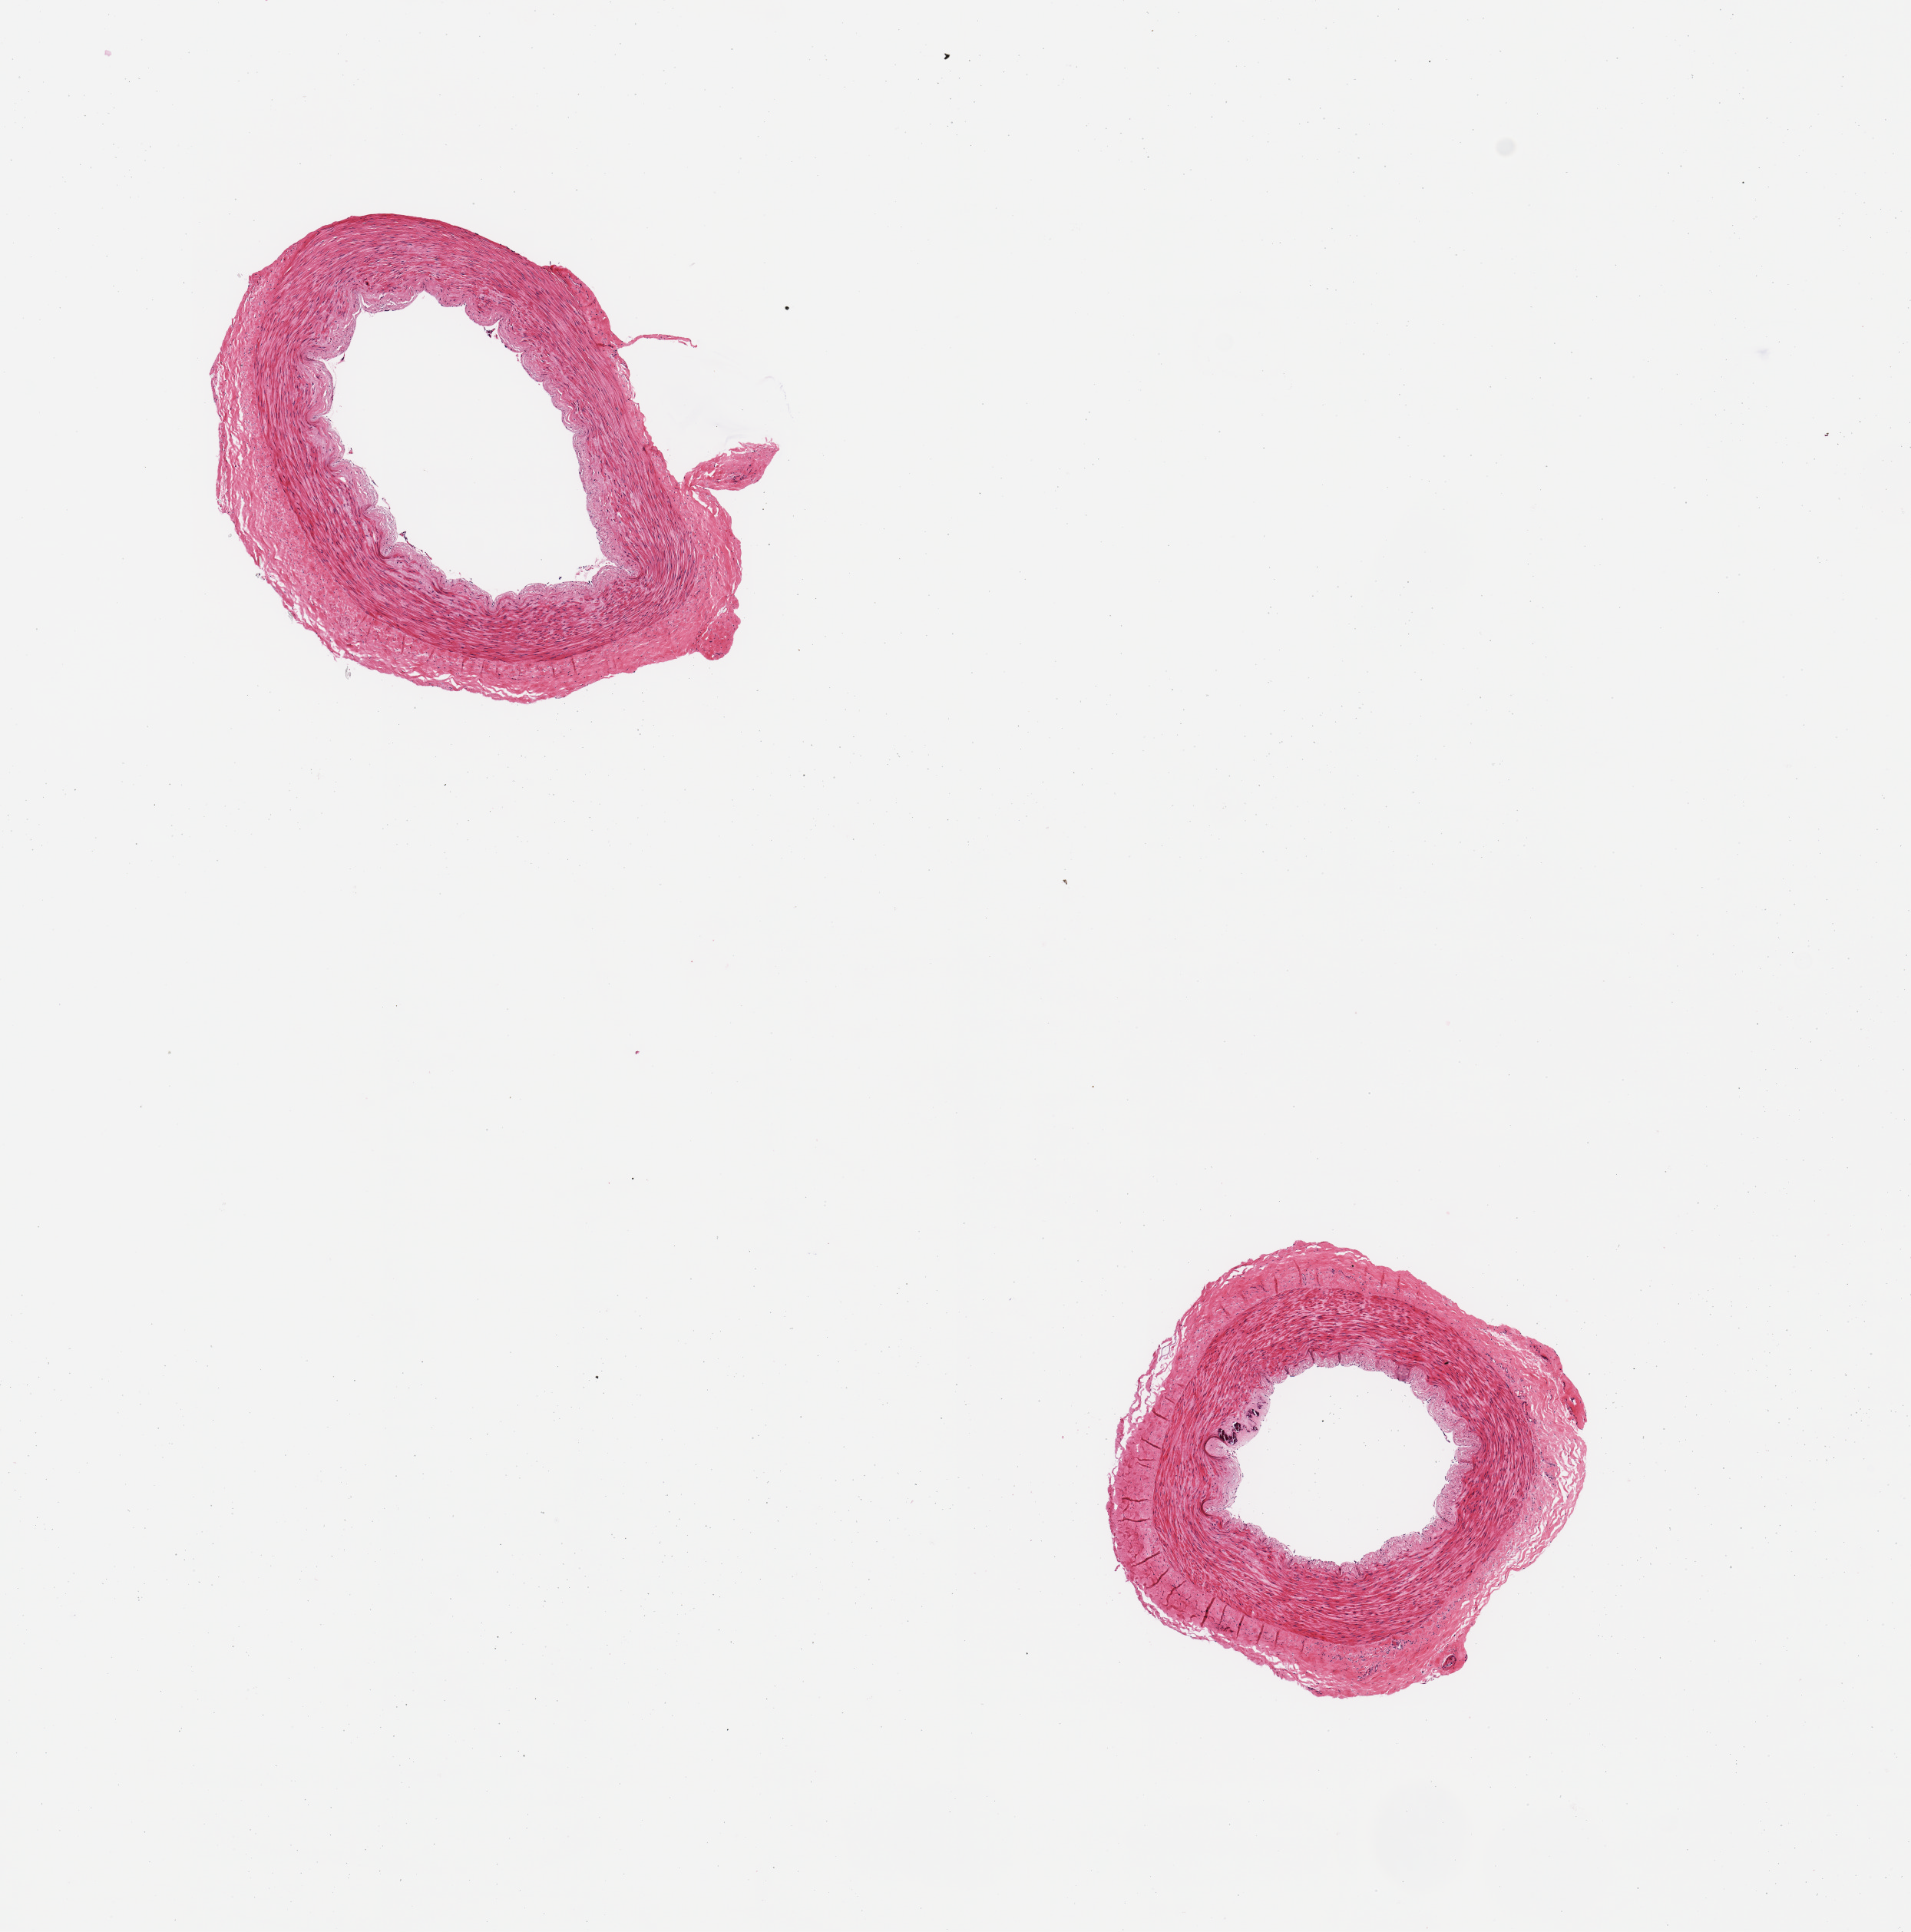
Digitized H&E-stained section, low-resolution overview of the scanned area, about 9.8 x 10.0 mm, PAXgene-fixed paraffin-embedded (PFPE) section, section of tibial artery (target tissue), tissue donor sample. Male donor.
Review note (as recorded): 2 pieces; focally calcified intima with minimal plaque; well trimmed.